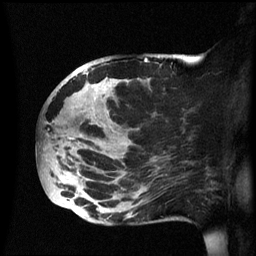
Breast MRI (dynamic contrast-enhanced), one sagittal slice. Position 28 of 60 along the scan axis. Dynamic contrast-enhanced series, image 2 of 3 at this slice position (ordered by acquisition). 1.5 T. TE 4.2 ms, TR 8.4 ms. 256 × 256 image matrix. Patient: female, 49 years.
Annotated regions visible in this slice (semi-automatic segmentation, software-assisted and operator-edited):
- analysis volume of interest (the breast-tissue region the enhancement analysis was run in; not a lesion): bounding box <39,54,174,225> (left, top, right, bottom; pixels)
- tumour enhancement mask (voxels above the 70 % enhancement threshold inside the analysis volume of interest): <67,72,110,213>